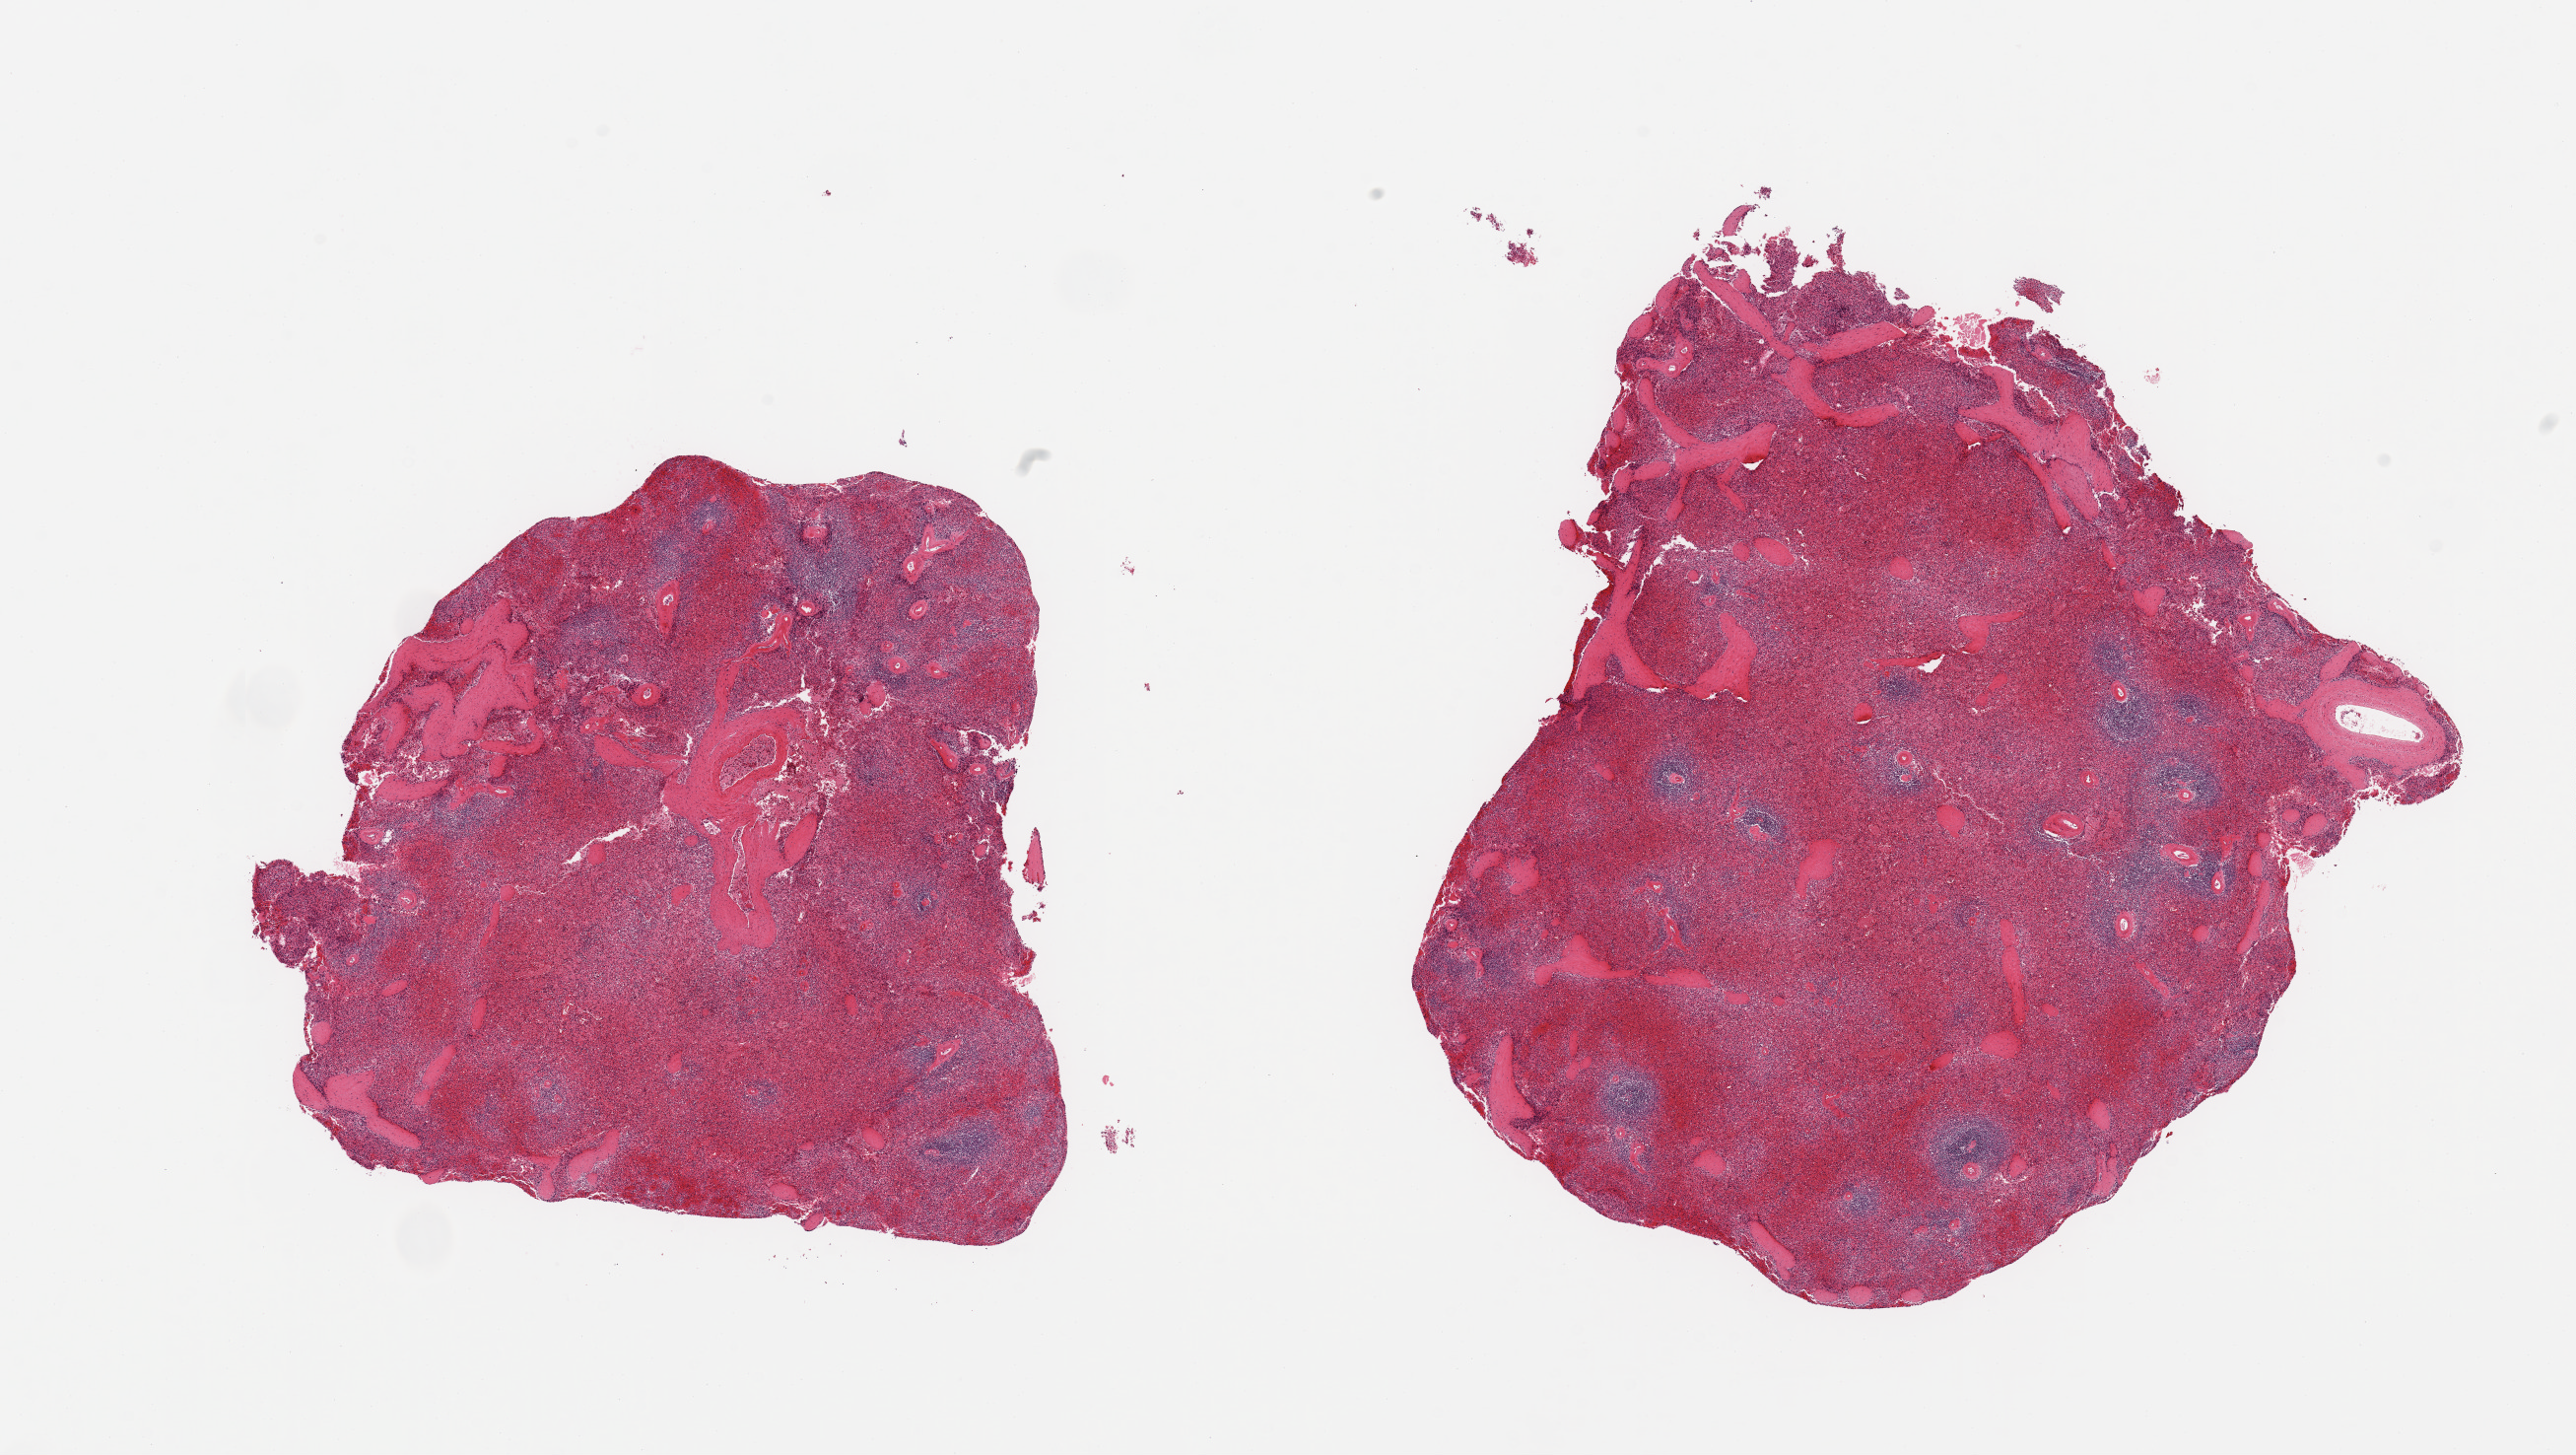
Digitized H&E-stained section — a low-resolution overview of the entire scanned area, about 20.7 x 11.7 mm. PAXgene-fixed, paraffin-embedded tissue. Section of spleen (target tissue). Tissue donor sample. Donor: male.
* pathologist's review note for this sample: 2 pieces, marked congestion